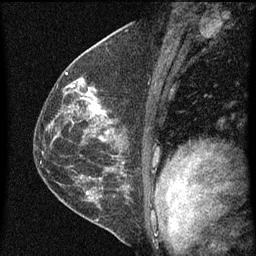
Breast MRI (dynamic contrast-enhanced), one sagittal slice. Slice 36 of 60 in the series (ordered by position). Dynamic contrast-enhanced series, image 2 of 4 at this slice position (ordered by acquisition). 1.5 T. TE 4.2 ms, TR 8 ms. 256 × 256 image matrix, field of view 180 × 180 mm. Patient: female, 48 years.
Annotated regions visible in this slice (semi-automatically segmented with operator editing):
- analysis volume of interest (the breast-tissue region the enhancement analysis was run in; not a lesion): bounding box <73,82,115,139> (left, top, right, bottom; pixels)
- tumour enhancement mask (voxels above the 70 % enhancement threshold inside the analysis volume of interest): <73,84,109,139>